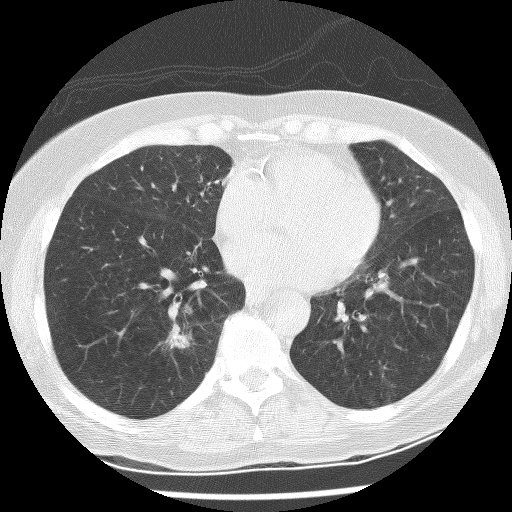
Low-dose screening chest CT, one axial slice. Position 101 of 247 along the scan axis. Reconstruction kernel BONE. 120 kVp. Lung window (W 1500 / L -600 HU). 2.5 mm slice thickness. 512 × 512 image matrix.
Annotated regions visible in this slice (manually delineated by an expert):
- lesion 1 (tumor, lower lobe of right lung): box from (x=165, y=324) to (x=190, y=349) px